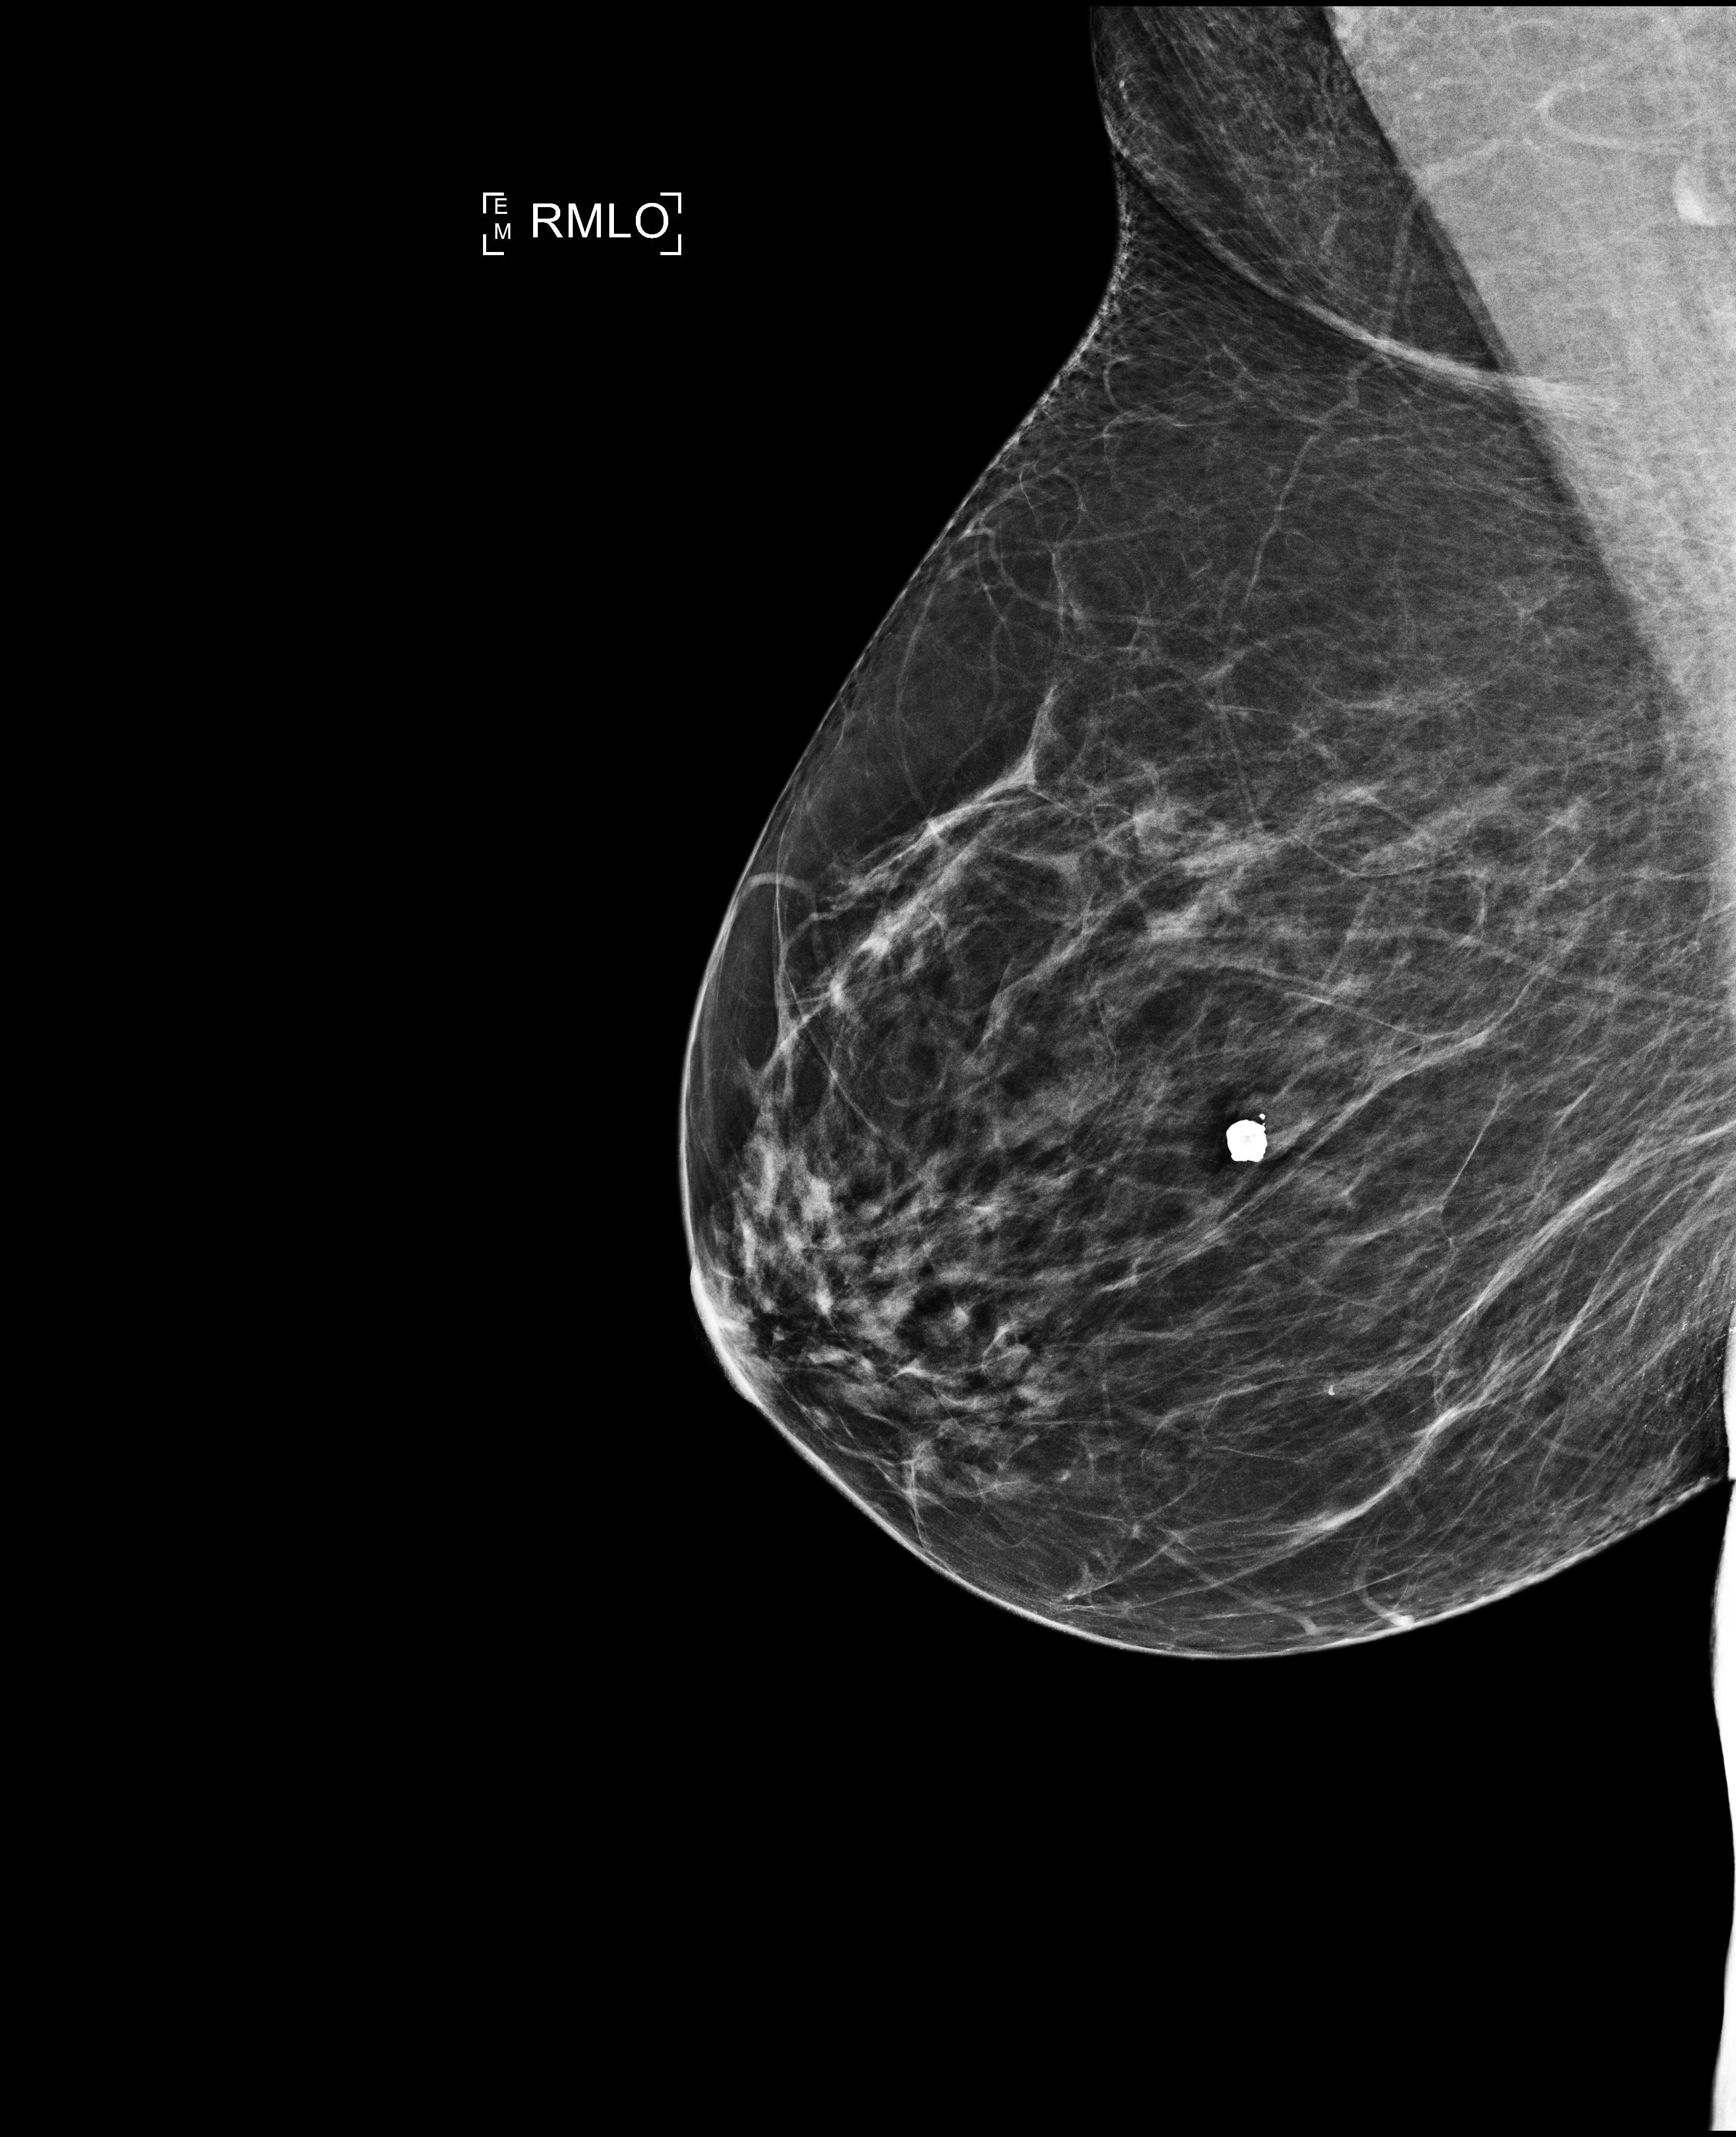
Digital mammogram (FFDM), right breast, MLO view, annual screening mammography examination. Patient: female, 64 years.
Breast density at the screening exam (both breasts): scattered fibroglandular densities (BI-RADS density category b). Final BI-RADS category for the screening round (tomosynthesis exam, both breasts): category 2. Recall: no recall after this screen.